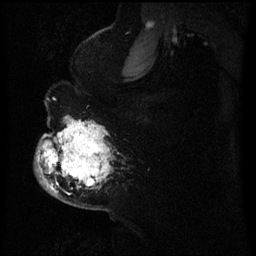
Breast MRI (dynamic contrast-enhanced), one sagittal slice. Position 45 of 60 along the scan axis. Dynamic contrast-enhanced series, image 2 of 3 at this slice position (ordered by acquisition). 1.5 T. TE 4.2 ms, TR 8 ms. 256 × 256 image matrix, field of view 200 × 200 mm. Female patient, age 50 years.
Annotated regions visible in this slice (semi-automatically segmented with operator editing):
- analysis volume of interest (the breast-tissue region the enhancement analysis was run in; not a lesion): bounding box <37,120,110,195> (left, top, right, bottom; pixels)
- tumour enhancement mask (voxels above the 70 % enhancement threshold inside the analysis volume of interest): <44,124,107,191>